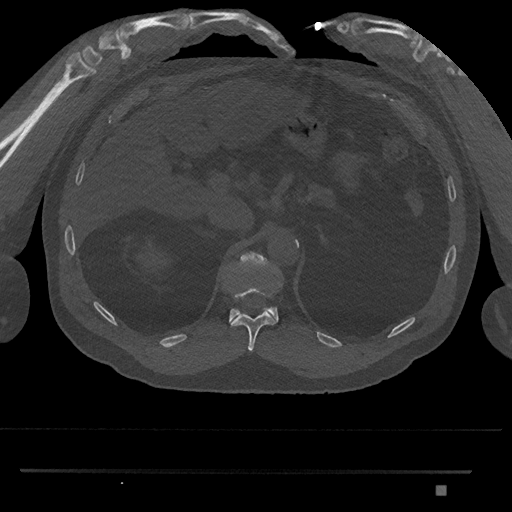
CT including the spine, one axial slice; slice 926 of 1134 in the series (ordered by position); 120 kVp; bone window (W 1800 / L 400 HU); 0.5 mm slice thickness; 512 × 512 image matrix. Patient: male, 65 years. Case-level facts recorded for this patient, not image findings: primary cancer: prostate.
Structures marked on this image (semi-automatic segmentation, software-assisted and operator-edited):
- T11 vertebra: box from (x=231, y=289) to (x=277, y=352) px
- T12 vertebra: (x=229, y=252)–(x=279, y=322)